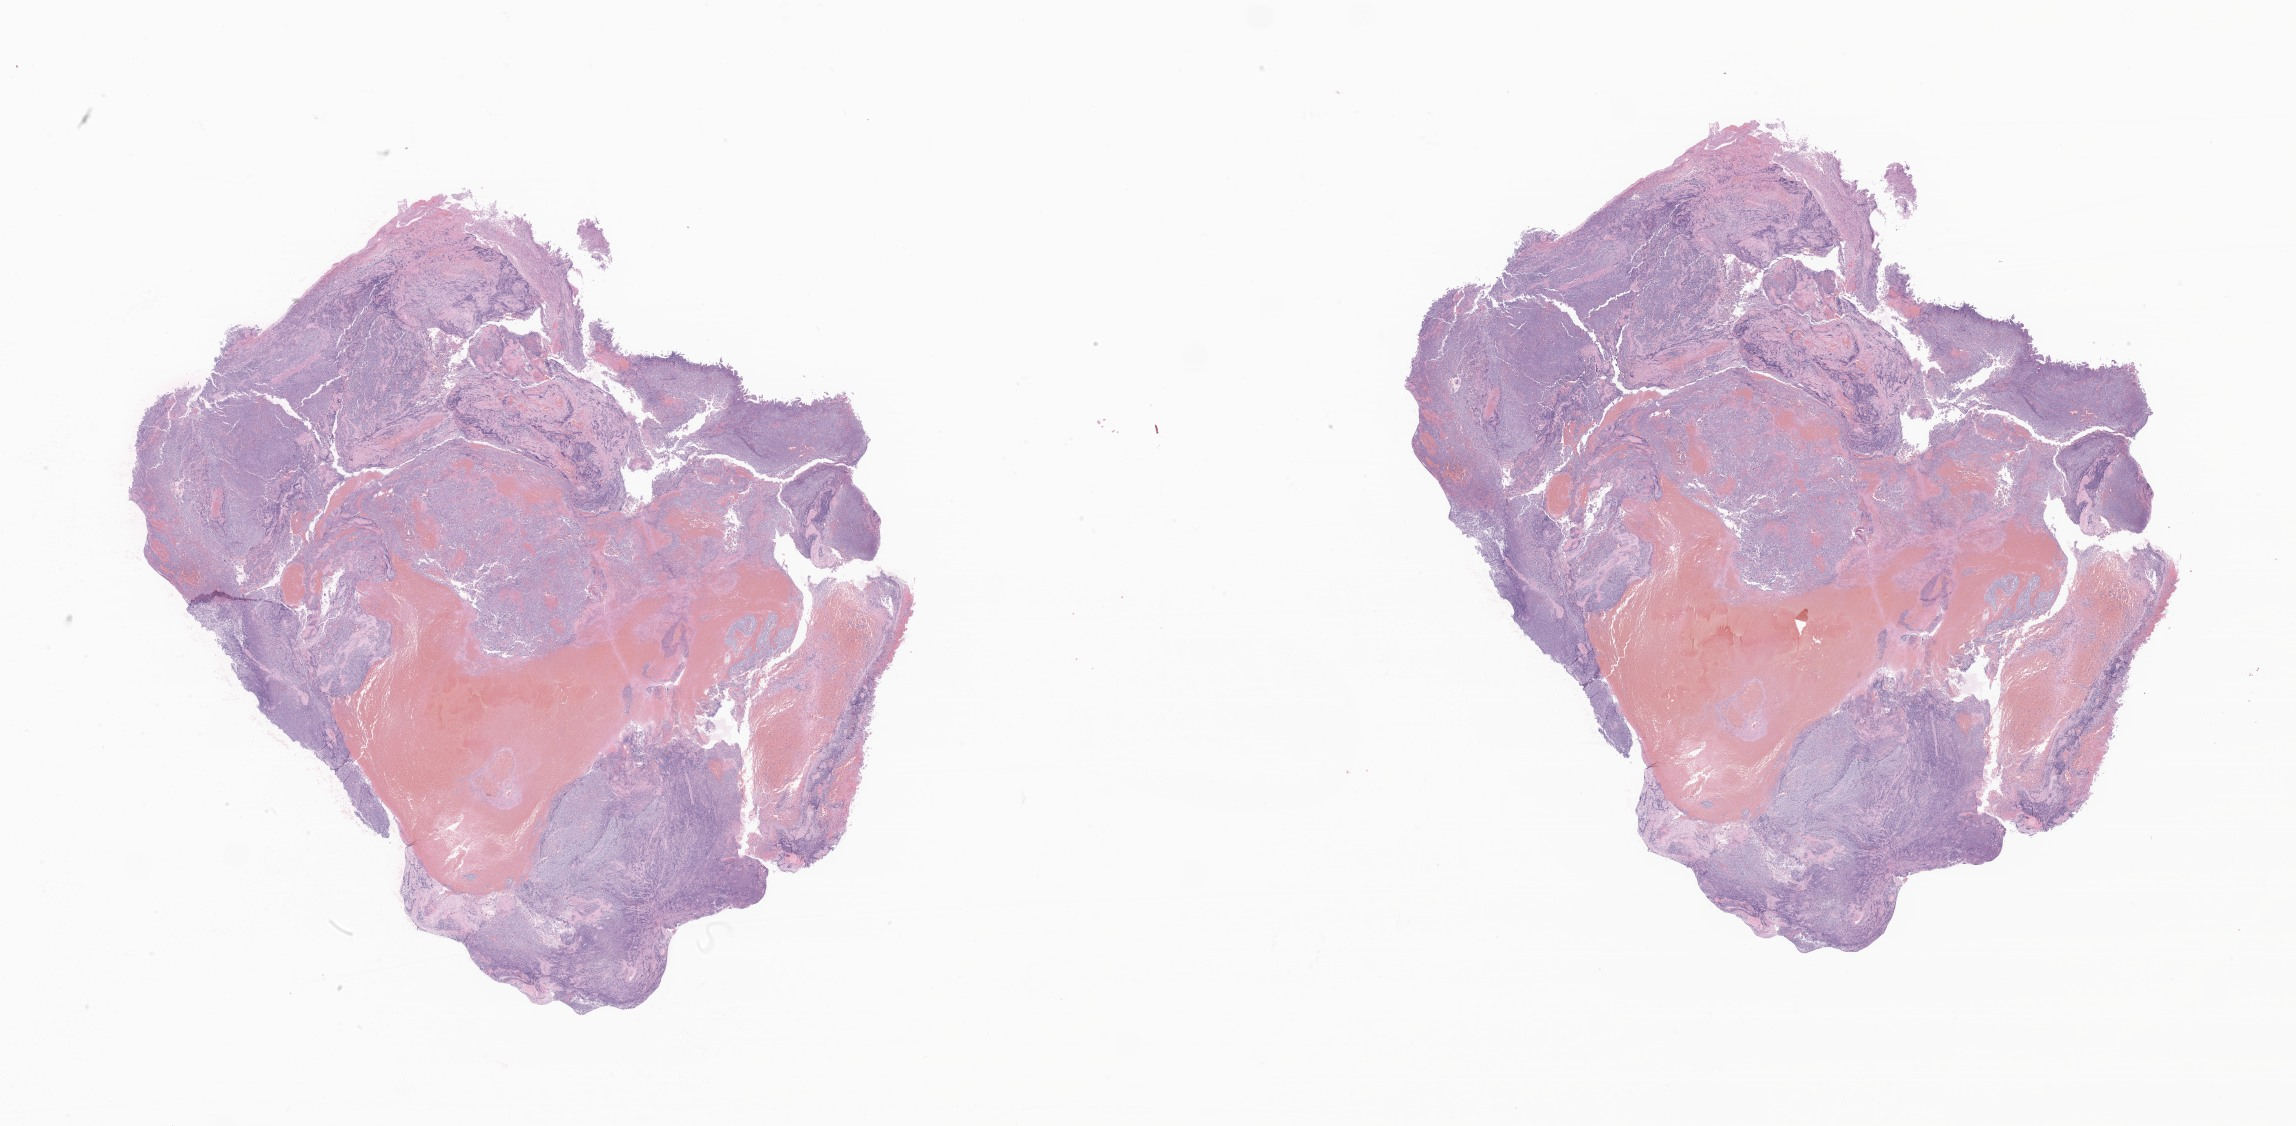
Whole-slide image, H&E stain of tumor tissue from the pineal gland — shown as a low-resolution overview of the whole scanned area (about 38.7 x 19.0 mm); FFPE section. Male patient, age 74 months (6 years 2 months).
Diagnosis (ICD-O-3 morphology term): Pineoblastoma.